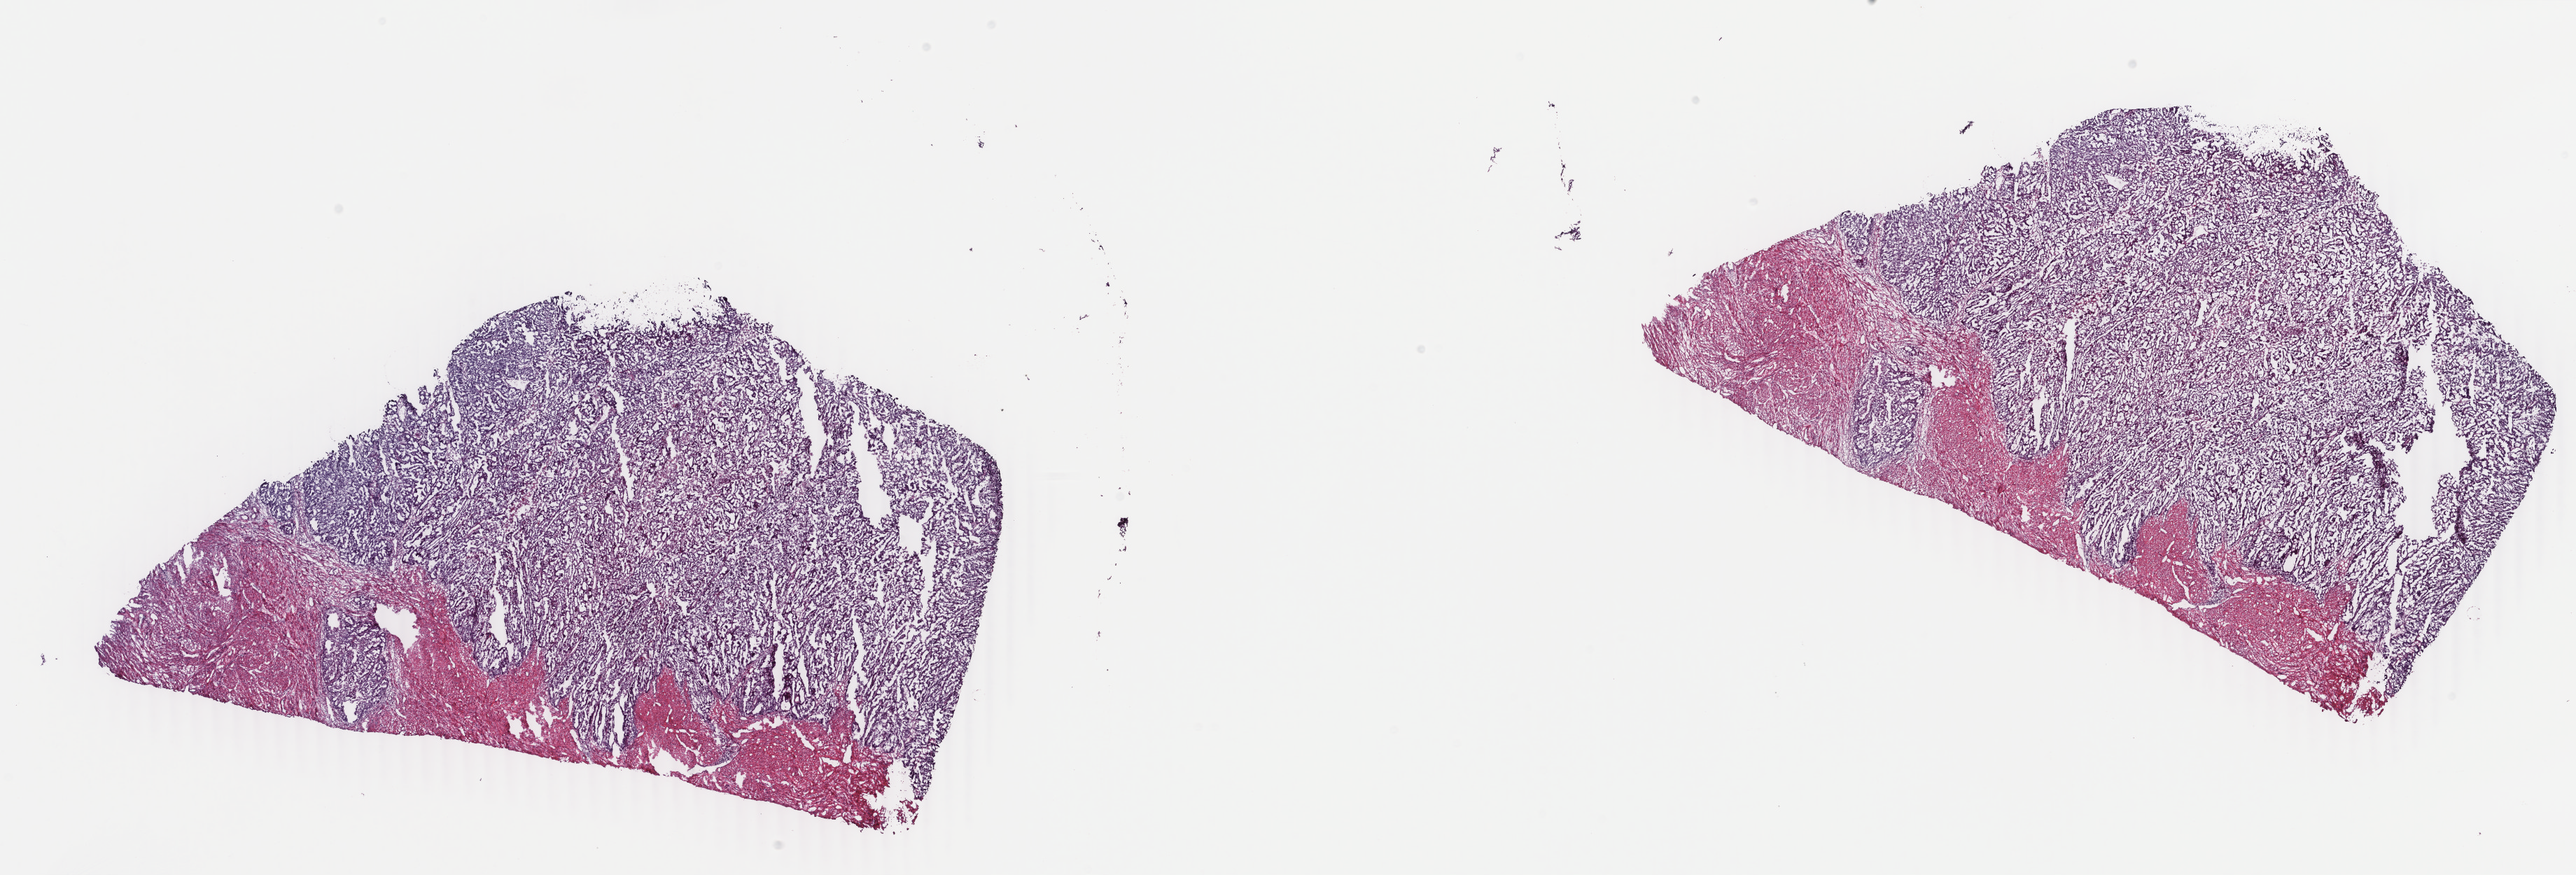
Whole-slide histology image, H&E-stained — low-resolution overview of the scanned area, about 29.3 x 9.9 mm, frozen section from the top of the tissue portion, uterus, primary tumour sample. Patient: female, age at initial diagnosis 66 years. Histologic grade: G3 (poorly differentiated). Pathologist review of this section (percent, as recorded): tumour cells 70%, tumour nuclei 65%, normal cells 20%, stromal cells 5%, necrosis 5%. Inflammatory infiltration, as recorded: lymphocyte infiltration 2%, monocyte infiltration 0%, neutrophil infiltration 4%.
* histologic diagnosis: Serous cystadenocarcinoma, NOS (endometrium)
* FIGO stage: IIIC